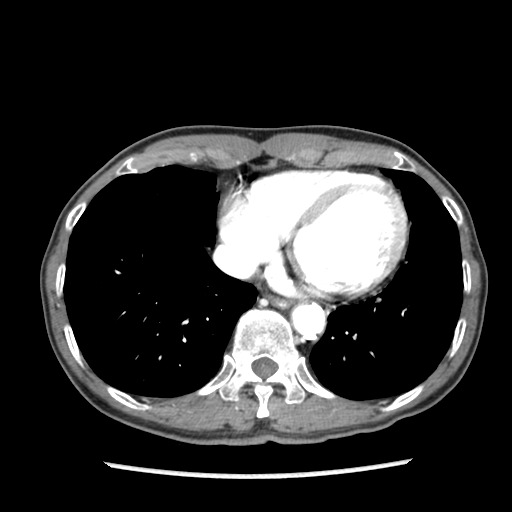
Contrast-enhanced abdominal CT (liver protocol), one axial slice. Slice 80 of 87 in the series (ordered by position). 140 kVp. Soft-tissue window (W 400 / L 40 HU). 512 × 512 image matrix. Case-level facts recorded for this patient, not image findings: diagnosis: hepatocellular carcinoma (patient treated with transarterial chemoembolisation; whether this scan precedes or follows treatment is not stated here); TNM stage (as recorded): Stage-IIIB; Child-Pugh class: A.
Structures marked on this image (semi-automatic segmentation, software-assisted and operator-edited):
- abdominal aorta: bounding box [x1, y1, x2, y2] px = [293, 304, 323, 338]